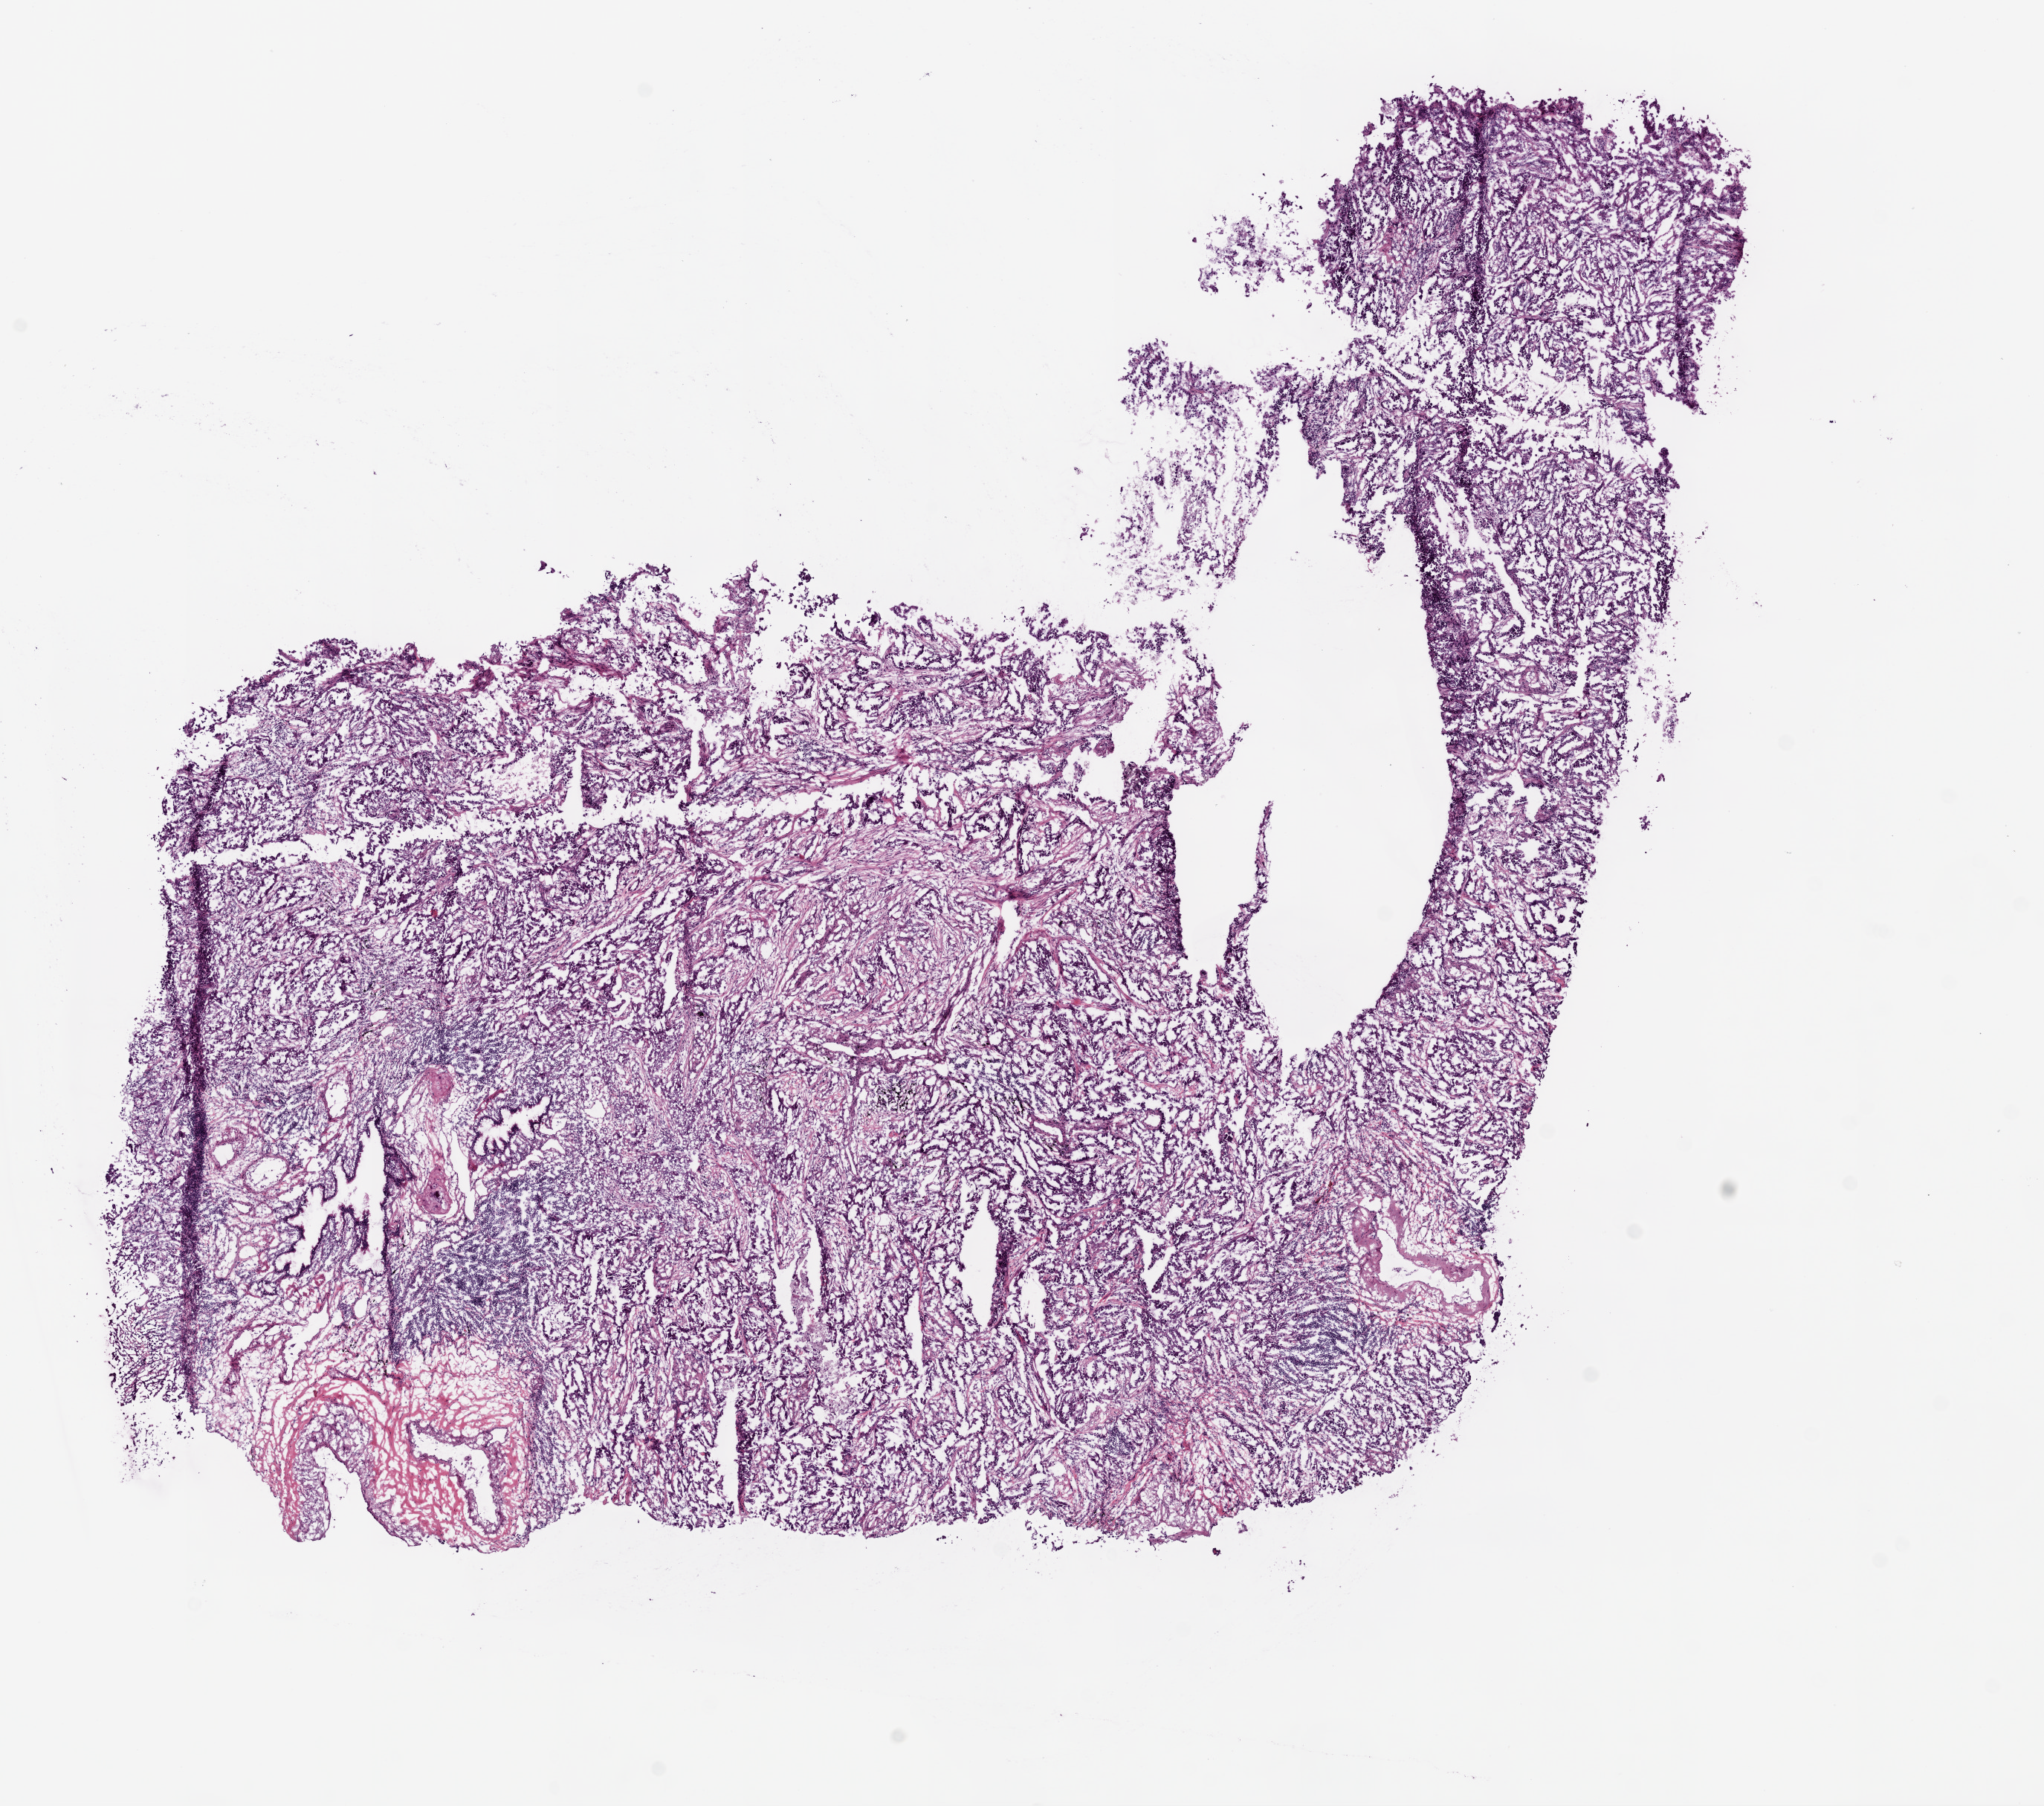
Whole-slide histology image, H&E-stained, low-resolution overview of the scanned area, about 11.0 x 9.7 mm (slide scanned at 20x); frozen section from the bottom of the tissue portion; primary tumour sample from the lung. Female, age 74 years at initial diagnosis. Composition of this section per pathologist review: tumour cells 89%, tumour nuclei 60%, normal cells 1%, stromal cells 10%, necrosis 0%.
AJCC pathologic stage: IA. Laterality: left. Histologic diagnosis: Adenocarcinoma, NOS (lower lobe, lung).